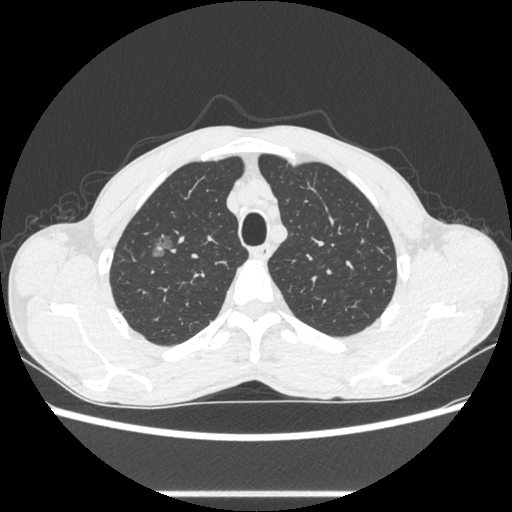
Chest CT, one axial slice. Position 480 of 600 along the scan axis. Reconstruction kernel STANDARD. Lung window (W 1500 / L -600 HU). 512 × 512 image matrix. Patient: male, 54 years. From the clinical record (not read from this slice): clinical TNM (as recorded): T1a N0 M0.
Outlined on this slice (rectangle marked by the reading radiologist):
- lung tumour (recorded histology: adenocarcinoma): bounding box (x1, y1, x2, y2) in pixels: (143, 224, 177, 267)